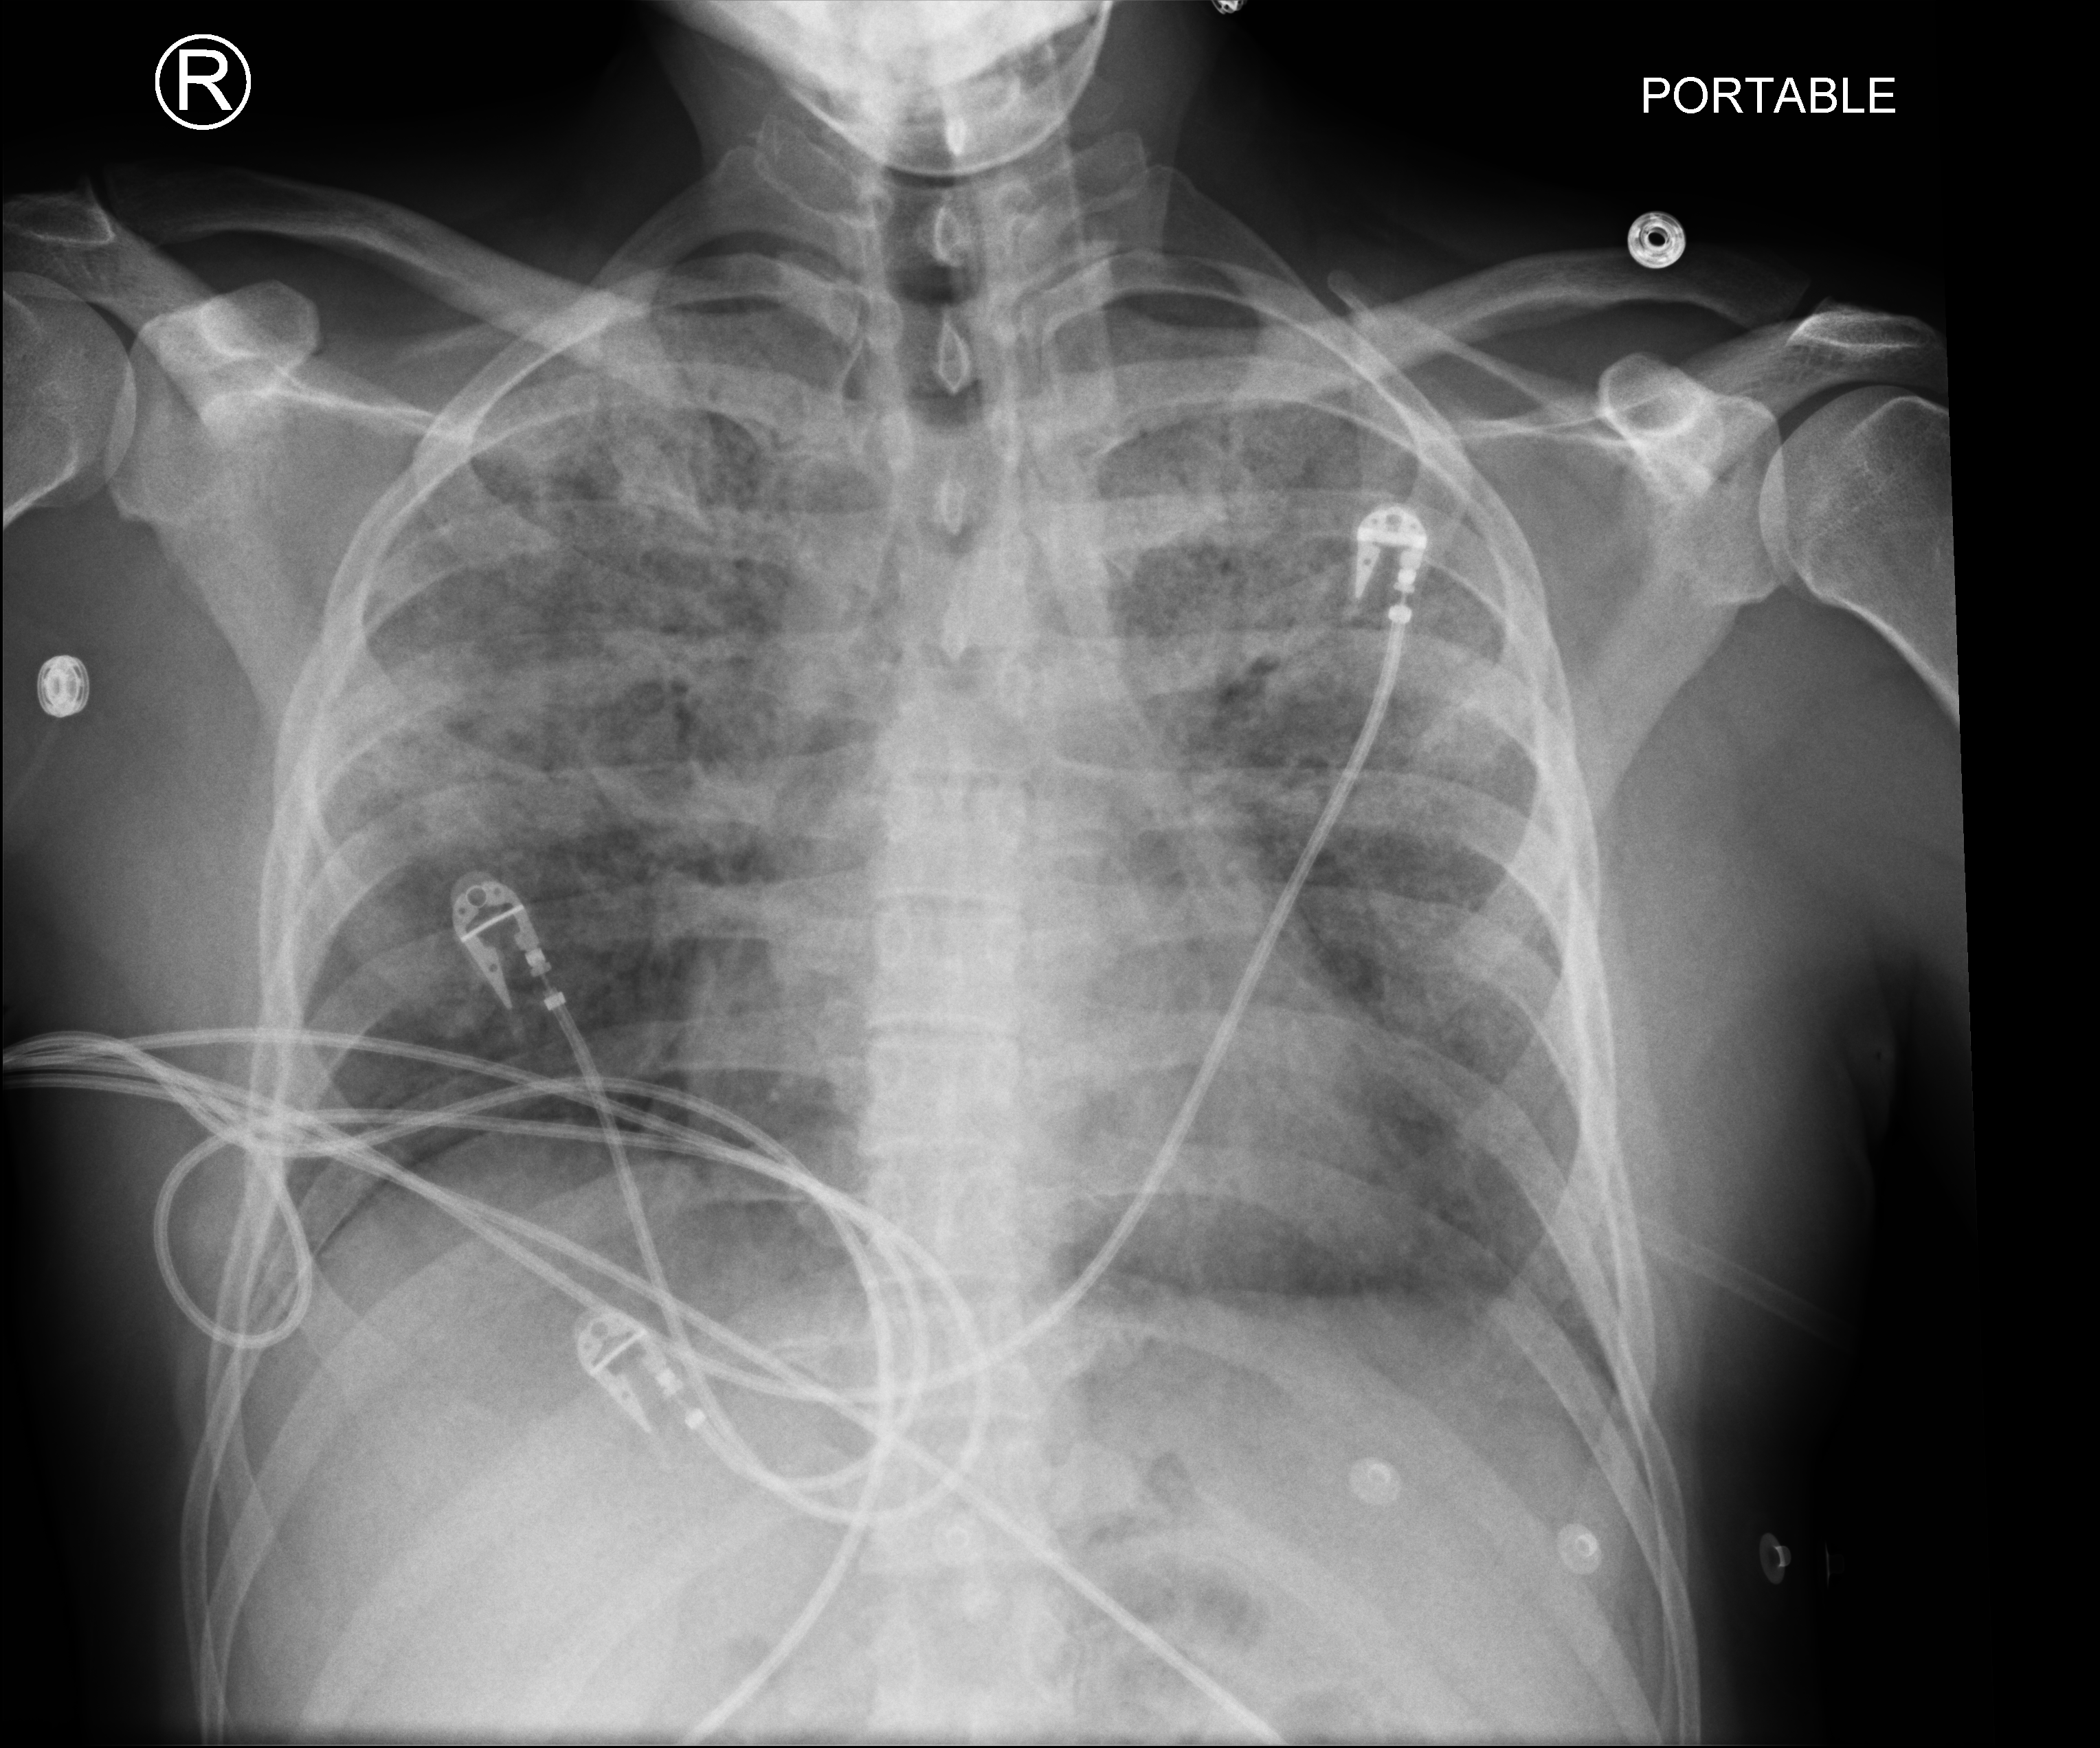
Portable chest radiograph; anteroposterior (AP) projection. Patient hospitalised with COVID-19; male, aged 18–59 years.
From the hospital-stay record, not from the radiograph (when in the stay this image was taken is not recorded):
- mechanically ventilated during this hospital stay: yes
- hypertension (admission record): no
- smoking status (admission record): never